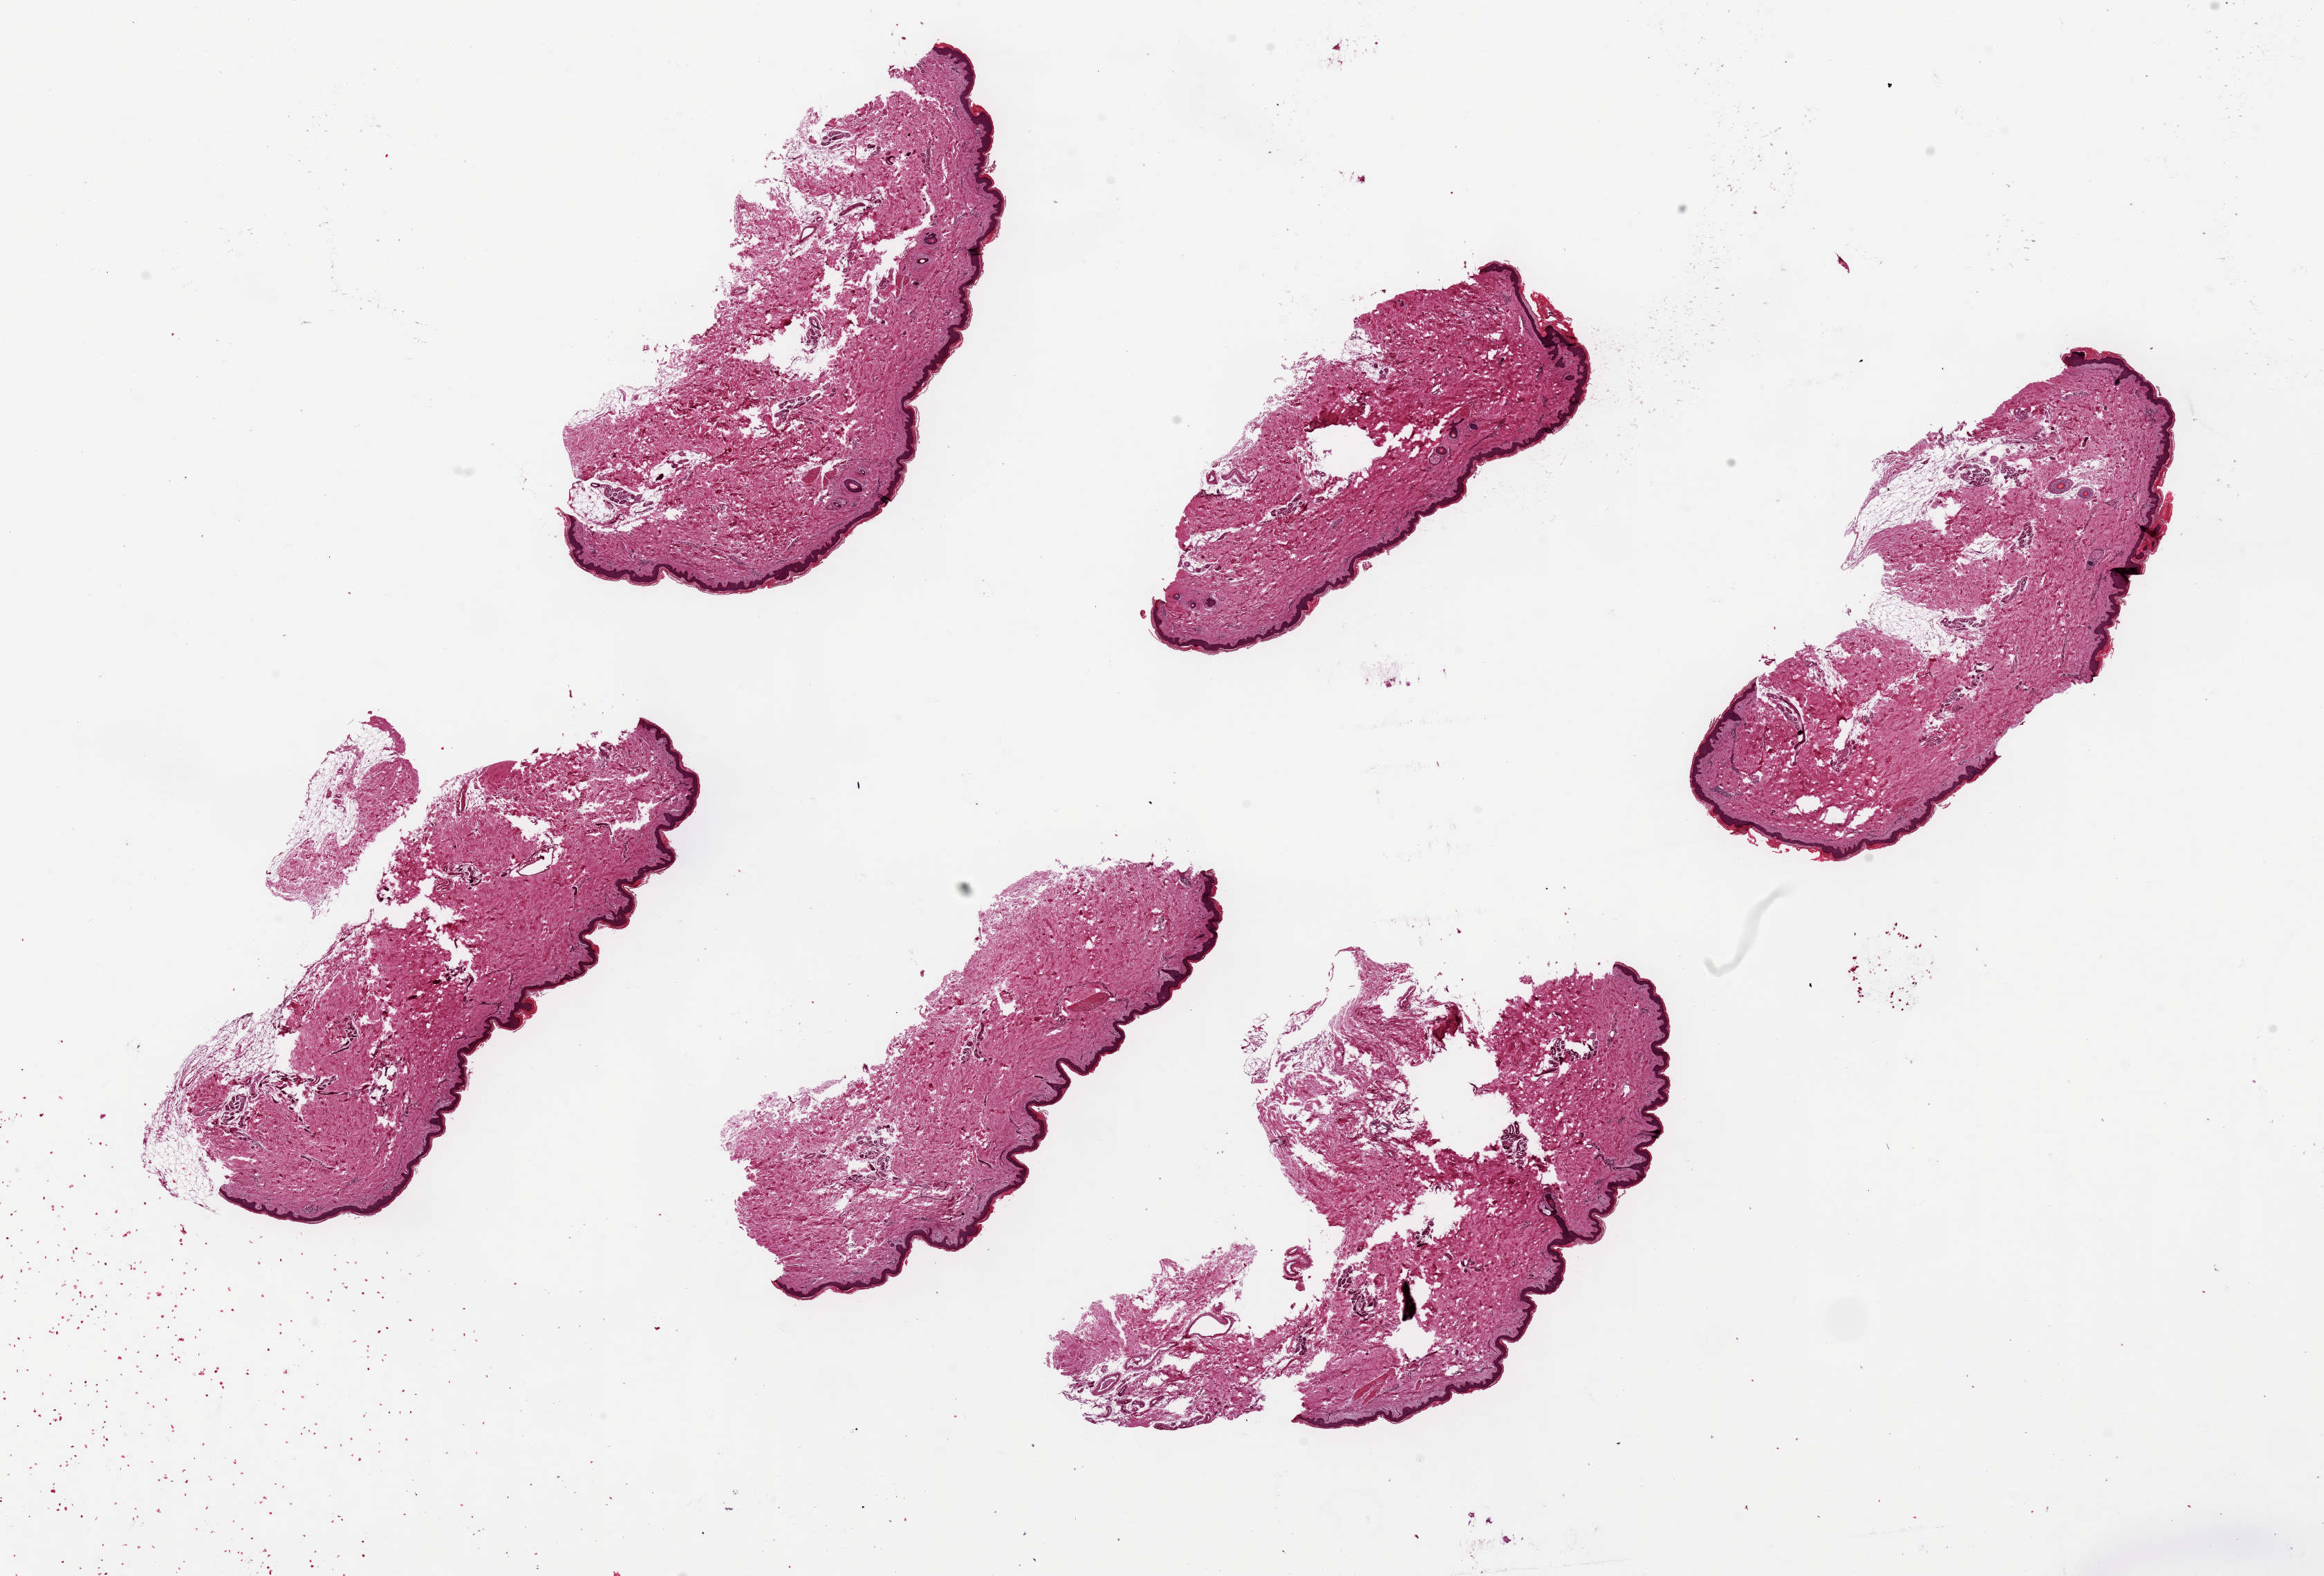
Whole-slide image, H&E stain, brightfield, shown as a low-resolution overview of the whole scanned area (about 26.6 x 18.0 mm, from a 20x scan). PAXgene-fixed paraffin-embedded (PFPE) section. Section of skin of lower leg (target tissue). Donor tissue sample.
* pathologist's review note for this sample: 6 pieces, ~7x2.5mm, squamous epithelium is ~3-5% of thickness